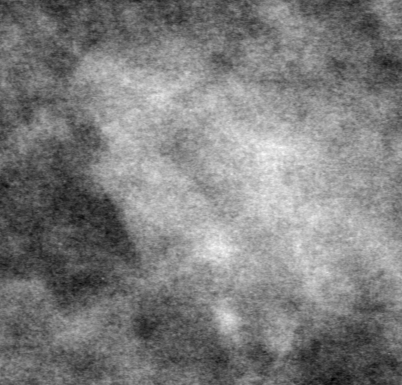
Region of interest cut from a scanned film mammogram (one marked finding), left breast, MLO view.
Mass, shape oval, margins obscured; BI-RADS assessment category 0; pathology (as recorded): benign.